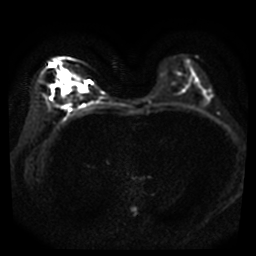
Breast MRI, one axial slice; position 20 of 40 along the scan axis; diffusion-weighted series; image 2 of 4 stored at this slice position (different b-values; order by instance number); 3 T; 5 mm slice thickness; 256 × 256 image matrix, field of view 320 × 320 mm. Female patient.
Annotated regions visible in this slice (outlined manually by an expert reader):
- tumour on diffusion-weighted imaging: bounding box [x1, y1, x2, y2] px = [56, 70, 74, 94]